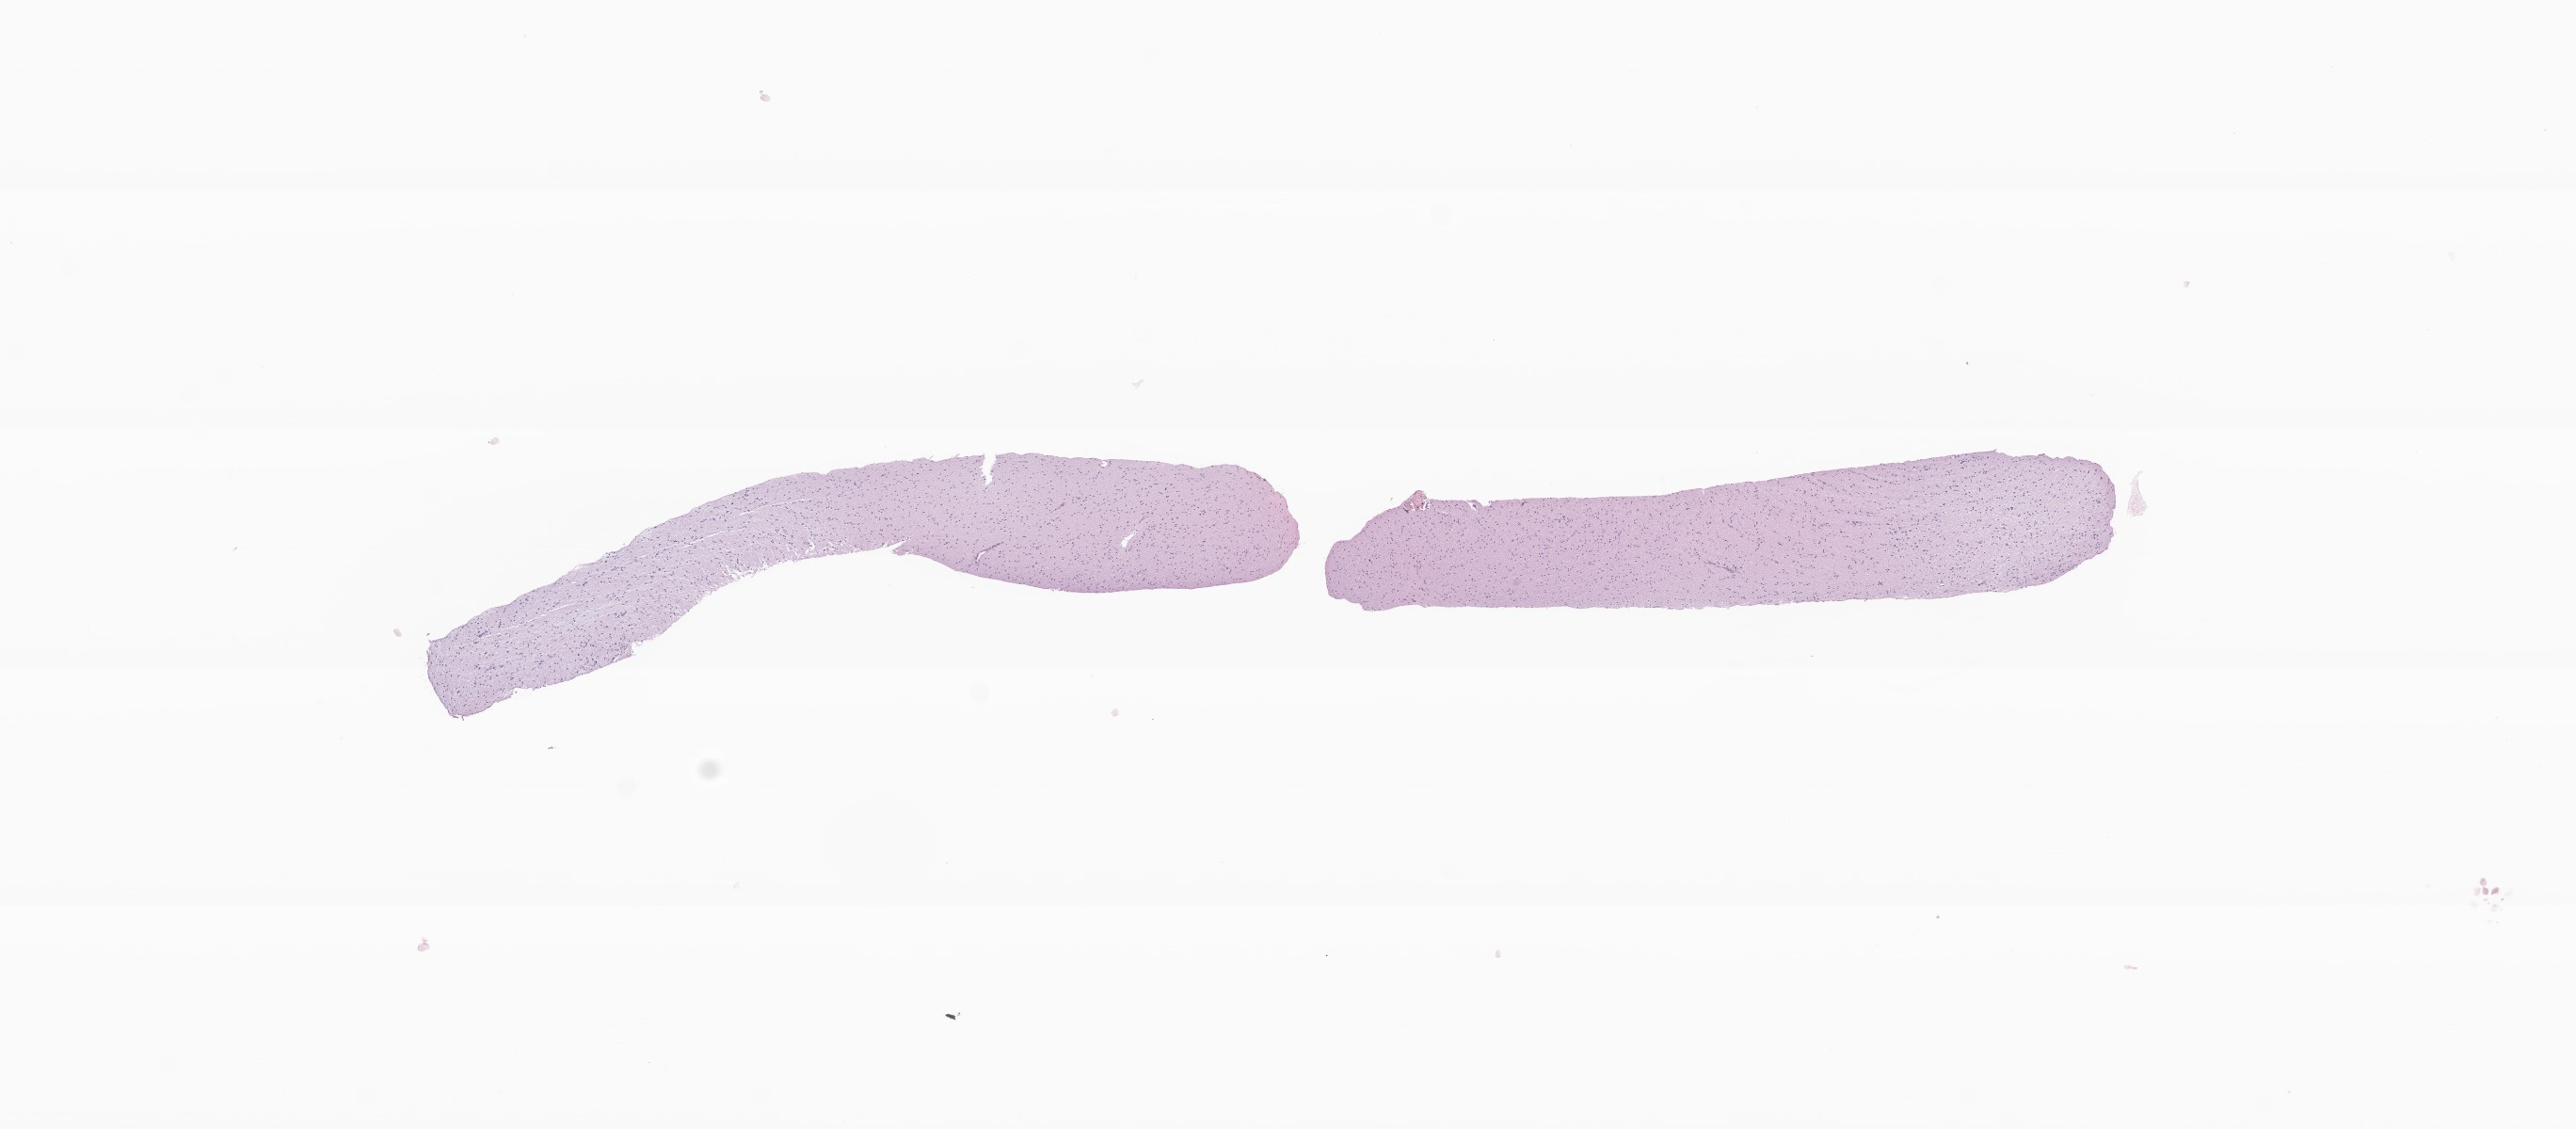
Whole-slide image, H&E stain of tumor tissue from the frontal lobe, low-resolution overview of the scanned area, about 11.5 x 5.0 mm. Formalin-fixed paraffin-embedded section. Patient: female, age 204 months (17 years).
• diagnosis (ICD-O-3 morphology term): Oligoastrocytoma, NOS